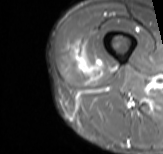
MRI of an extremity soft-tissue mass, one axial slice. Slice 12 of 61 in the series (ordered by position). STIR. MR volume resampled by the dataset authors to the PET/CT grid (not the native acquisition matrix). 163 × 154 image matrix, field of view 159 × 150 mm. Male patient. Case-level facts recorded for this patient, not image findings: histological type: poorly differentiated synovial sarcoma; grade: high; site of the primary tumour: right buttock.
Annotated regions visible in this slice (expert contour drawn on MRI and transferred to this co-registered scan by the dataset authors):
- gross tumour volume including surrounding oedema: box from (x=73, y=43) to (x=101, y=74) px